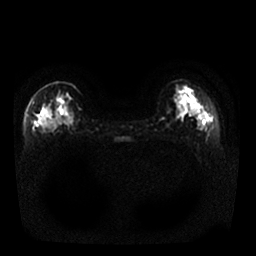
Breast MRI, one axial slice; slice 9 of 25 in the series (ordered by position); diffusion-weighted series; image 2 of 4 stored at this slice position (different b-values; order by instance number); 1.5 T; 4 mm slice thickness; 256 × 256 image matrix, field of view 340 × 340 mm. Female patient.
Structures marked on this image (expert manual segmentation):
- tumour on diffusion-weighted imaging: box from (x=41, y=116) to (x=53, y=132) px